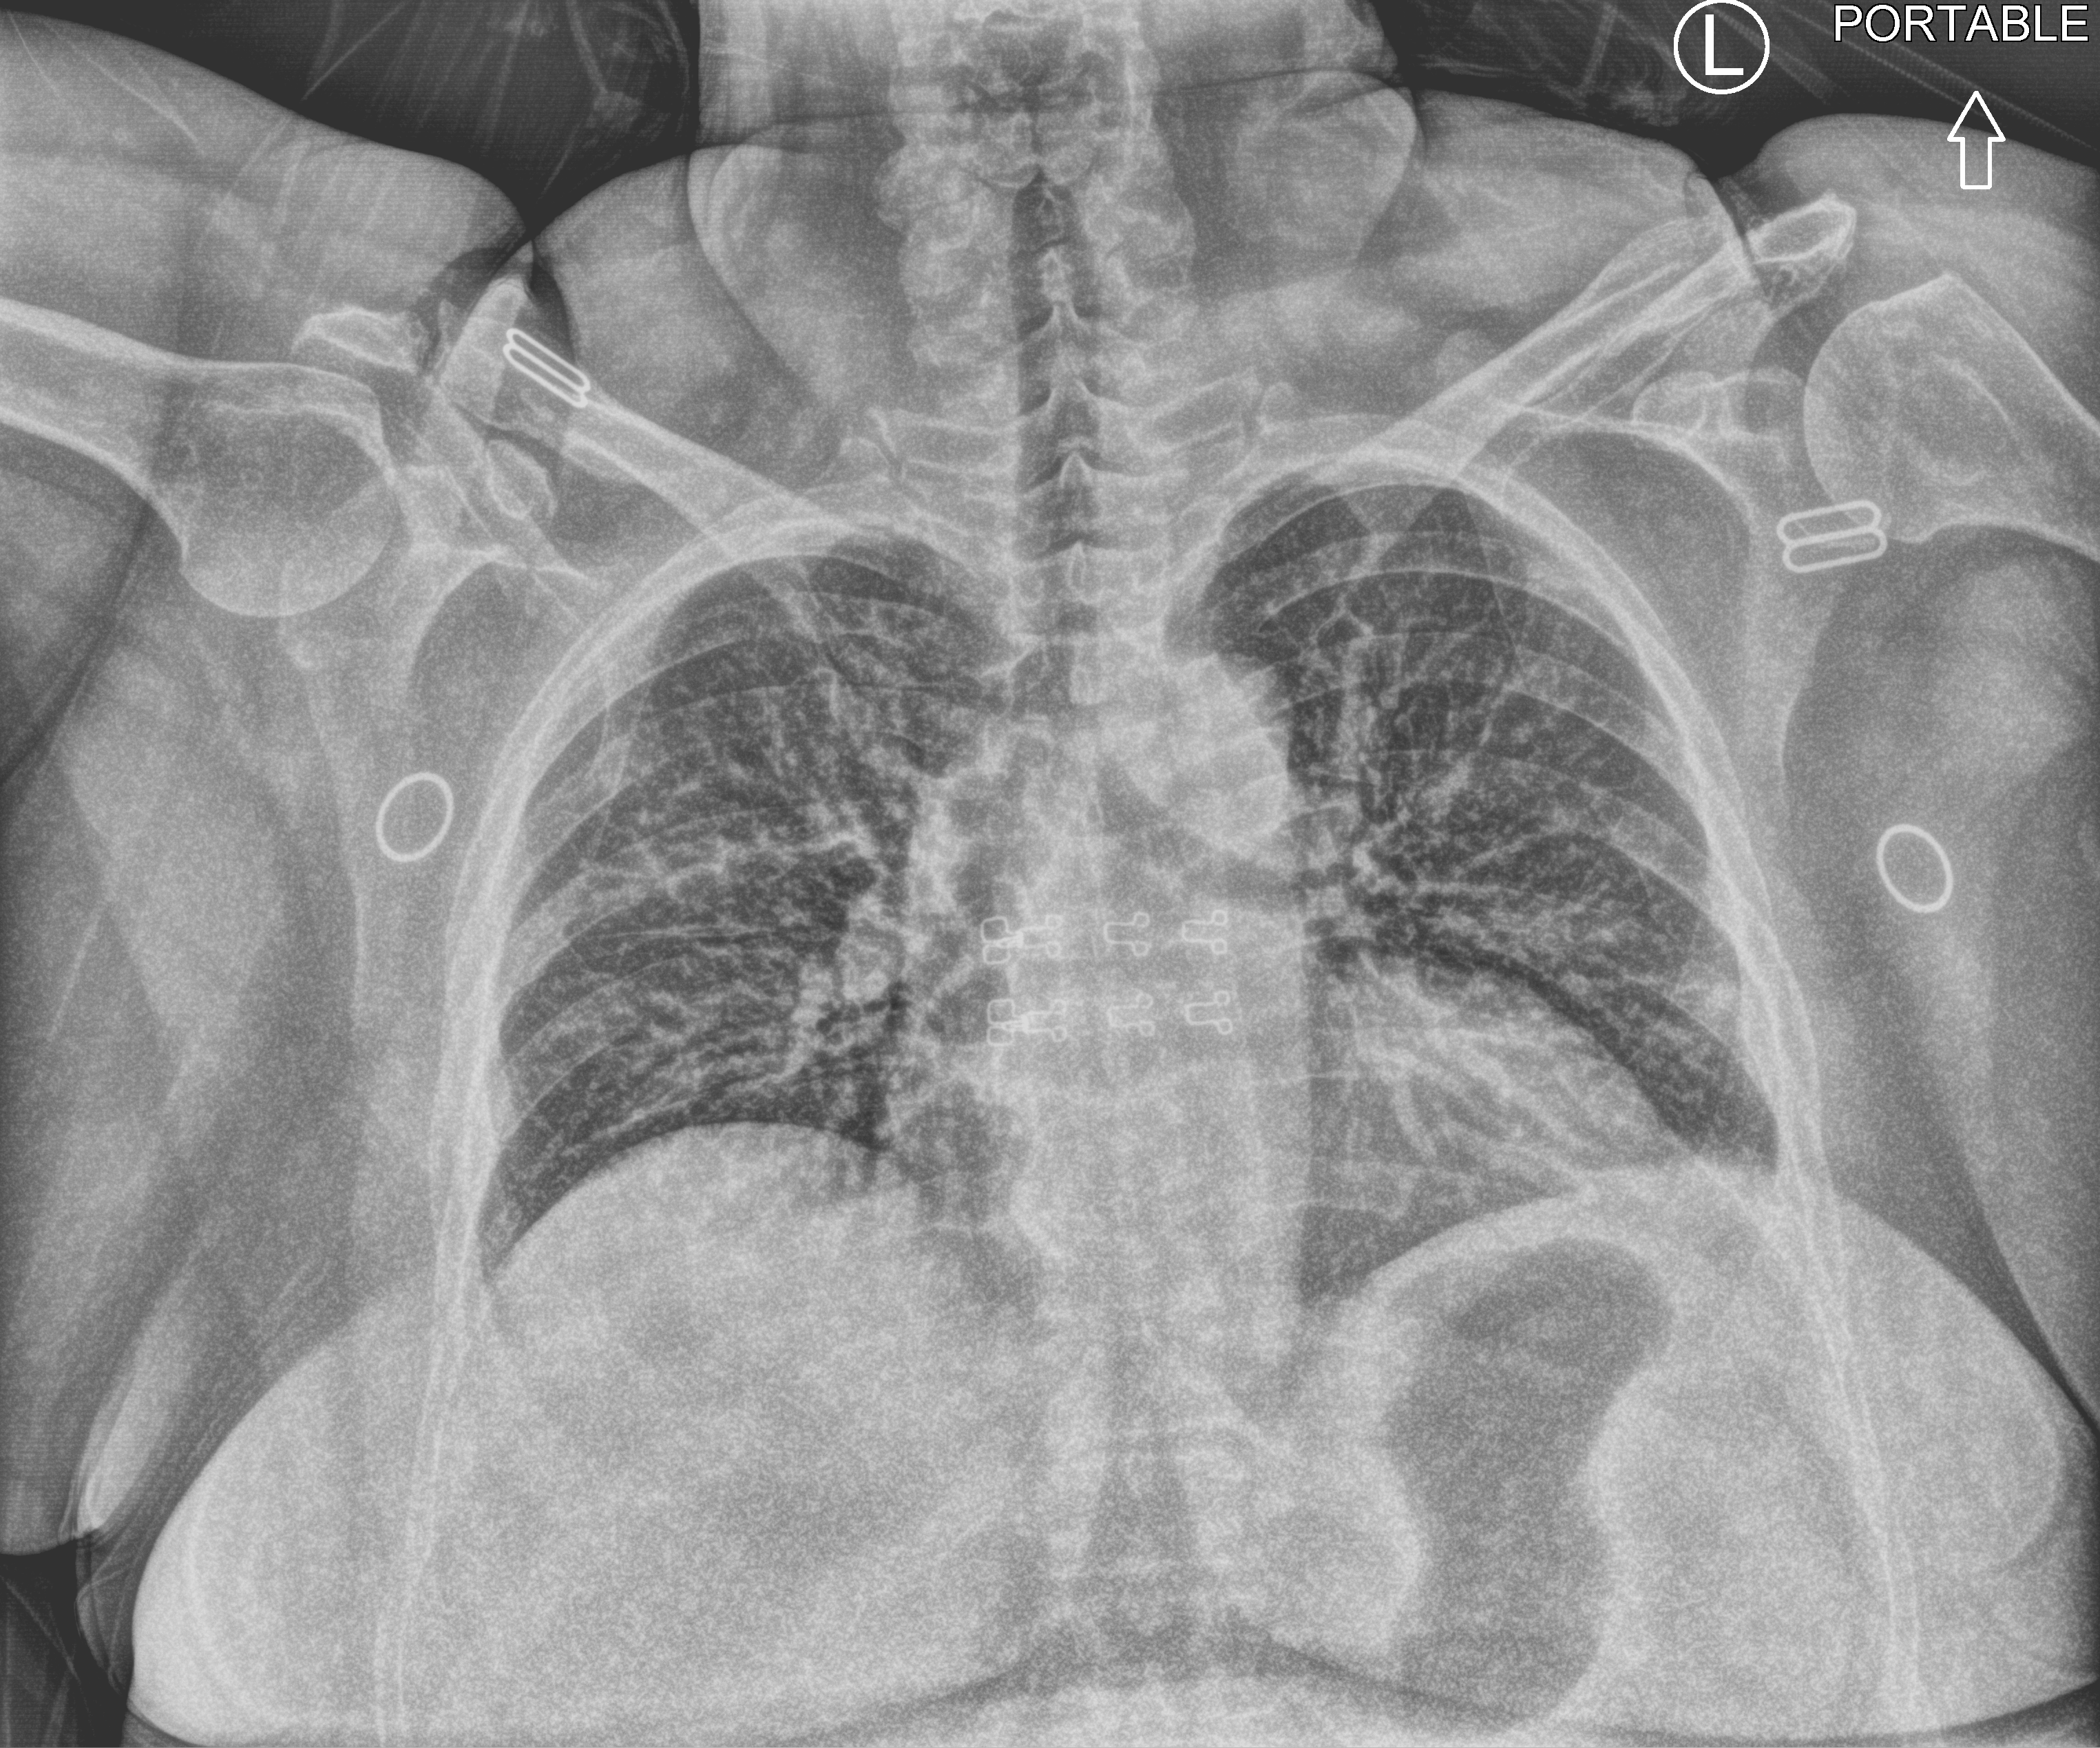
Chest X-ray (portable); anteroposterior (AP) projection. Female patient hospitalised with COVID-19, age 60–74 years.
Admission-level facts for this patient (not findings on this image; timing relative to this image not recorded):
- admitted to intensive care during this hospital stay: no
- mechanically ventilated during this hospital stay: no
- length of hospital stay: 1 day